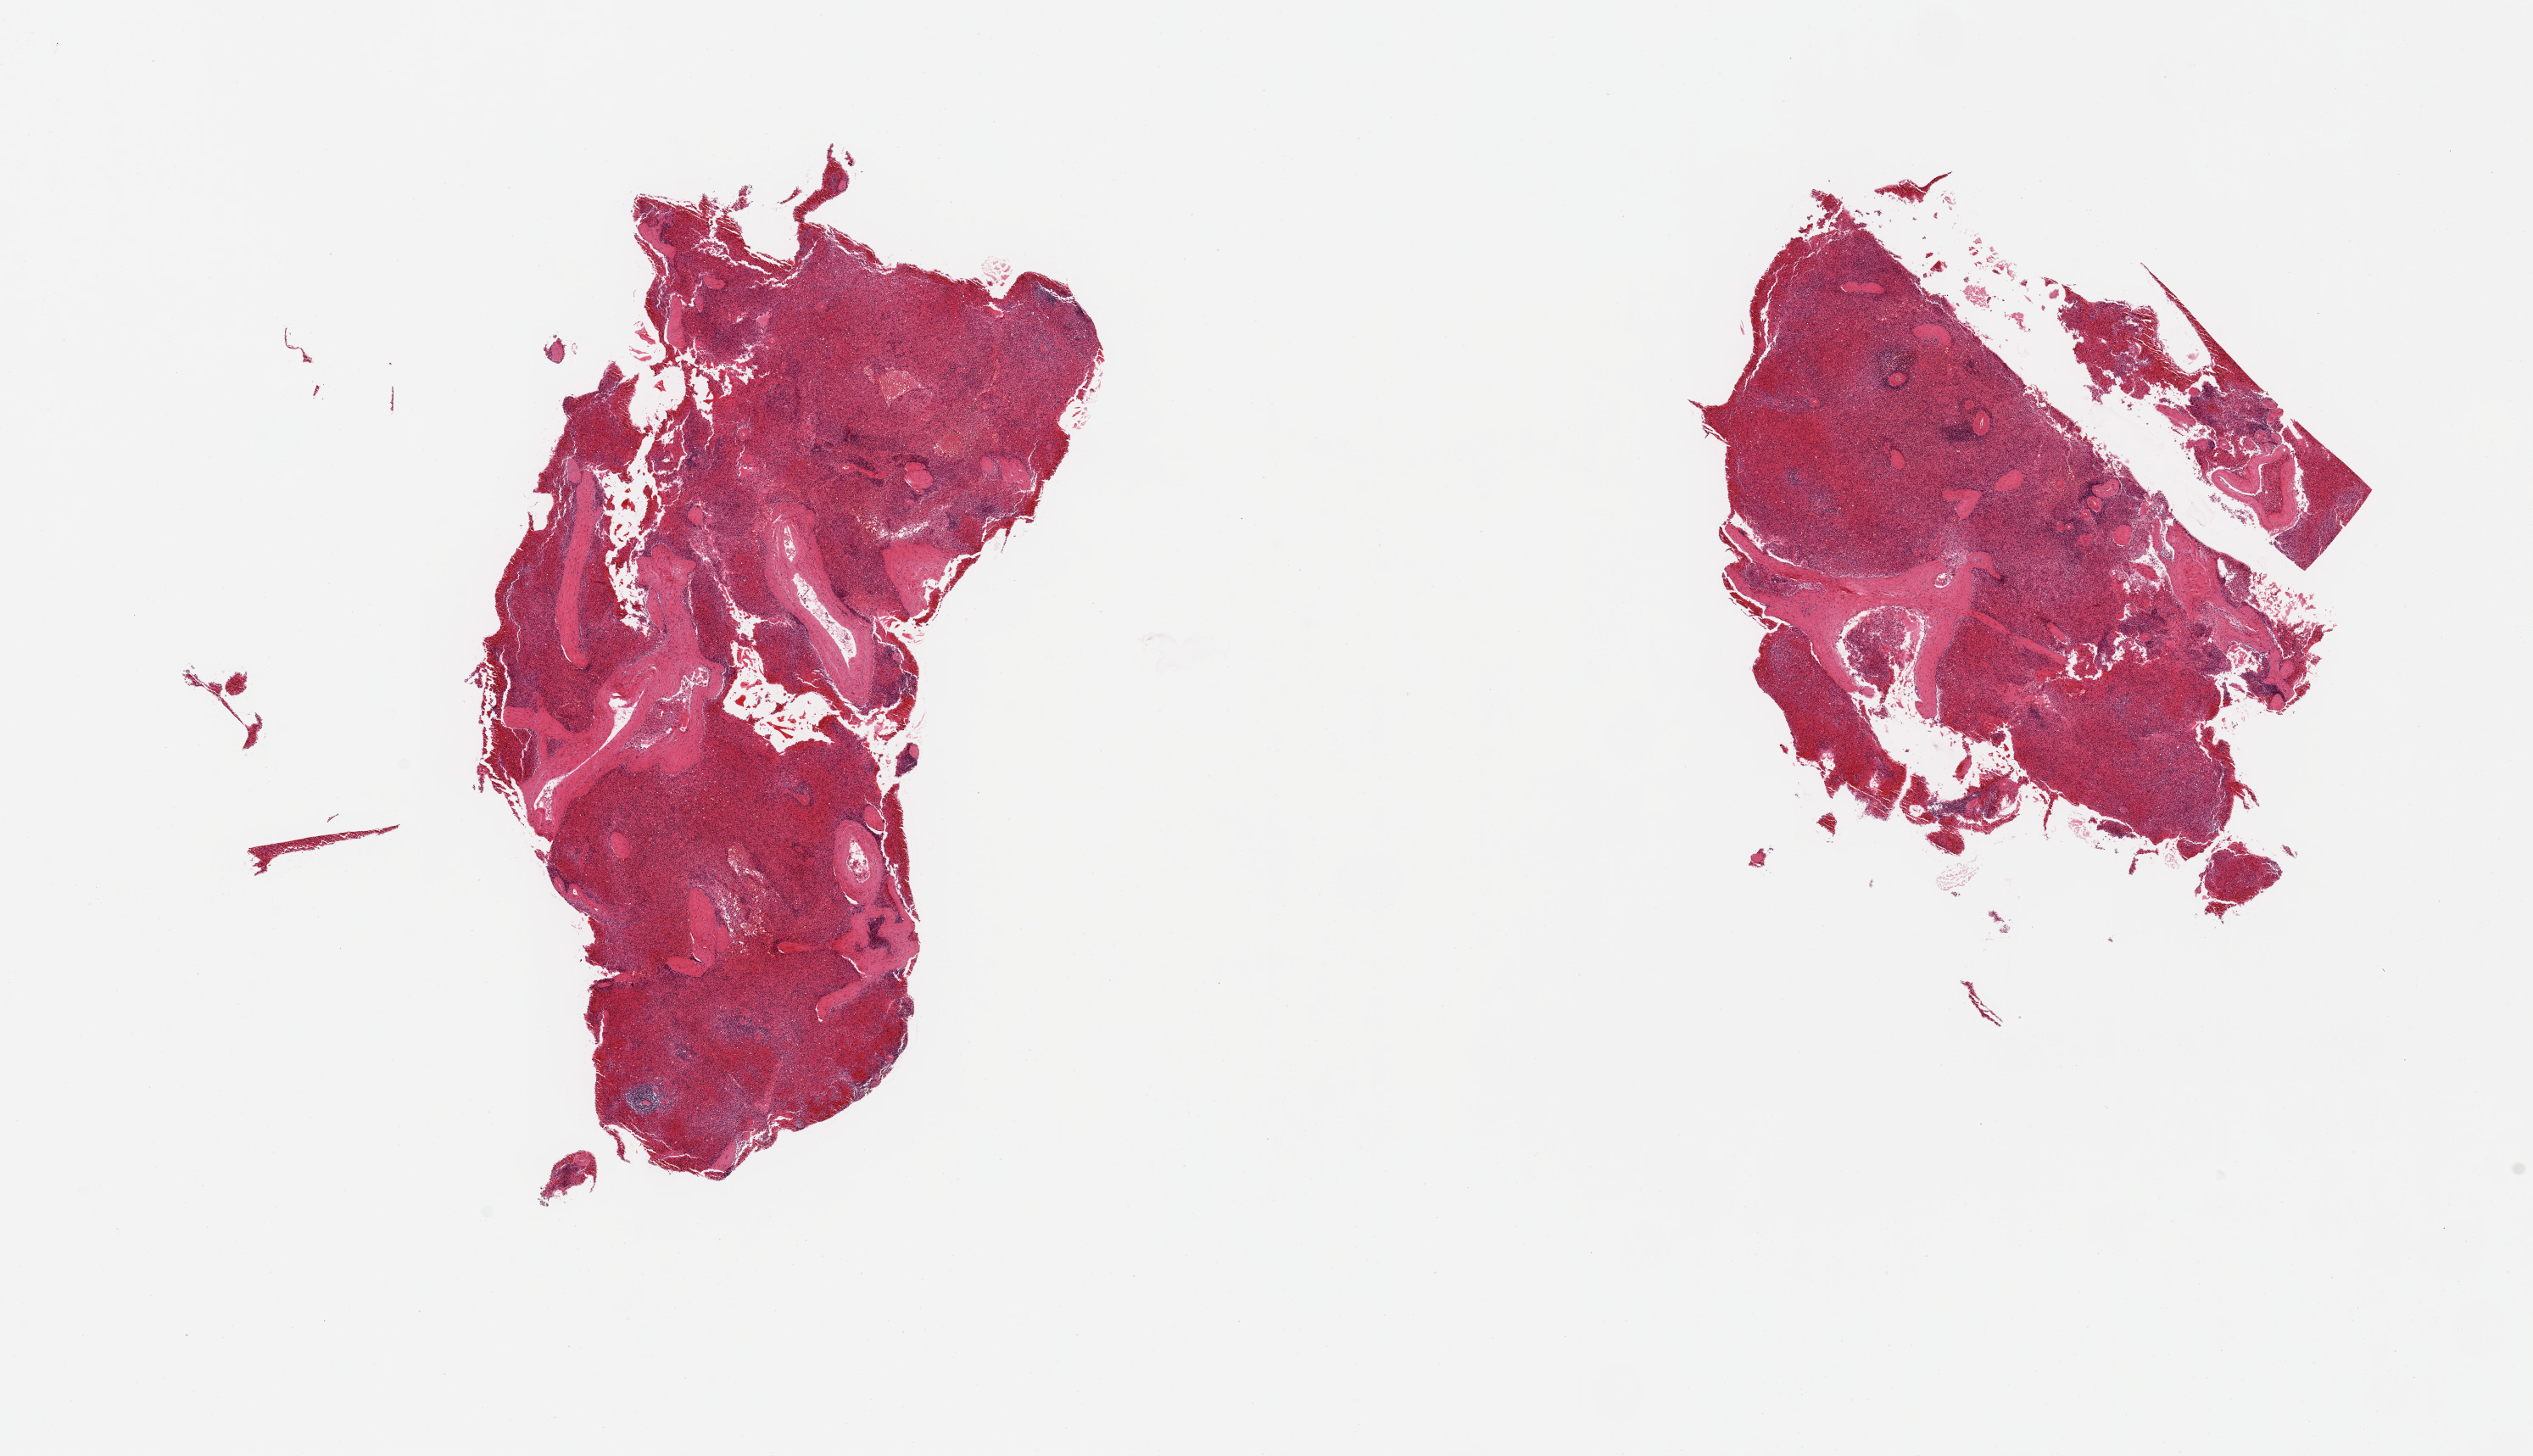
H&E whole-slide image, brightfield — whole scanned area (about 23.6 x 13.6 mm) shown as a low-resolution overview; PAXgene-fixed paraffin-embedded (PFPE) section; section of spleen (target tissue); donor tissue sample. Donor sex: male.
Reviewer comment on this tissue sample: 2 pieces; severe congestion; fragmented.